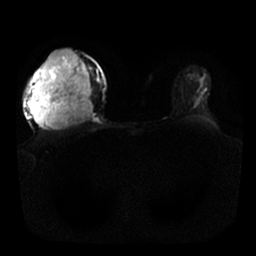
Breast MRI, one axial slice. Position 18 of 25 along the scan axis. Diffusion-weighted series; image 2 of 4 stored at this slice position (different b-values; order by instance number). 1.5 T. 256 × 256 image matrix. Female patient.
Outlined on this slice (manually delineated by an expert):
- tumour on diffusion-weighted imaging: bounding box [x1, y1, x2, y2] px = [32, 49, 95, 130]